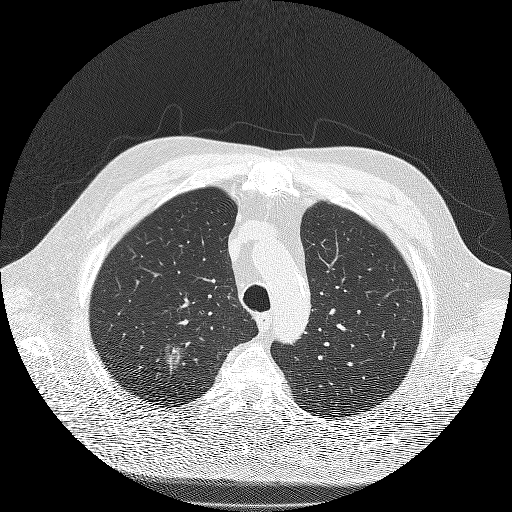
Low-dose screening chest CT, one axial slice; position 150 of 180 along the scan axis; reconstruction kernel FC51; lung window (W 1500 / L -600 HU); 512 × 512 image matrix, field of view 385 × 385 mm.
Structures marked on this image (expert manual segmentation):
- lesion 1 (tumor, upper lobe of right lung): bounding box (x1, y1, x2, y2) in pixels: (168, 348, 180, 372)